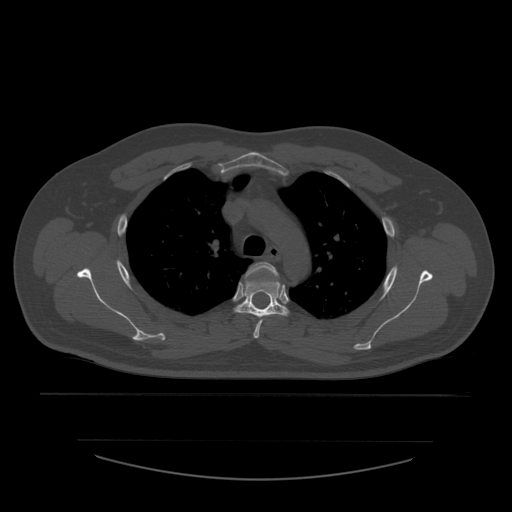
CT including the spine, one axial slice. Reconstruction kernel STANDARD. 120 kVp. Bone window (W 1800 / L 400 HU). 1.25 mm slice thickness. 512 × 512 image matrix, field of view 441 × 441 mm. Patient age 44 years. Case-level facts recorded for this patient, not image findings: primary cancer: soft tissue sarcoma.
Outlined on this slice (semi-automatically segmented with operator editing):
- T3 vertebra: bounding box [x1, y1, x2, y2] px = [246, 262, 281, 339]
- T4 vertebra: [235, 279, 289, 338]